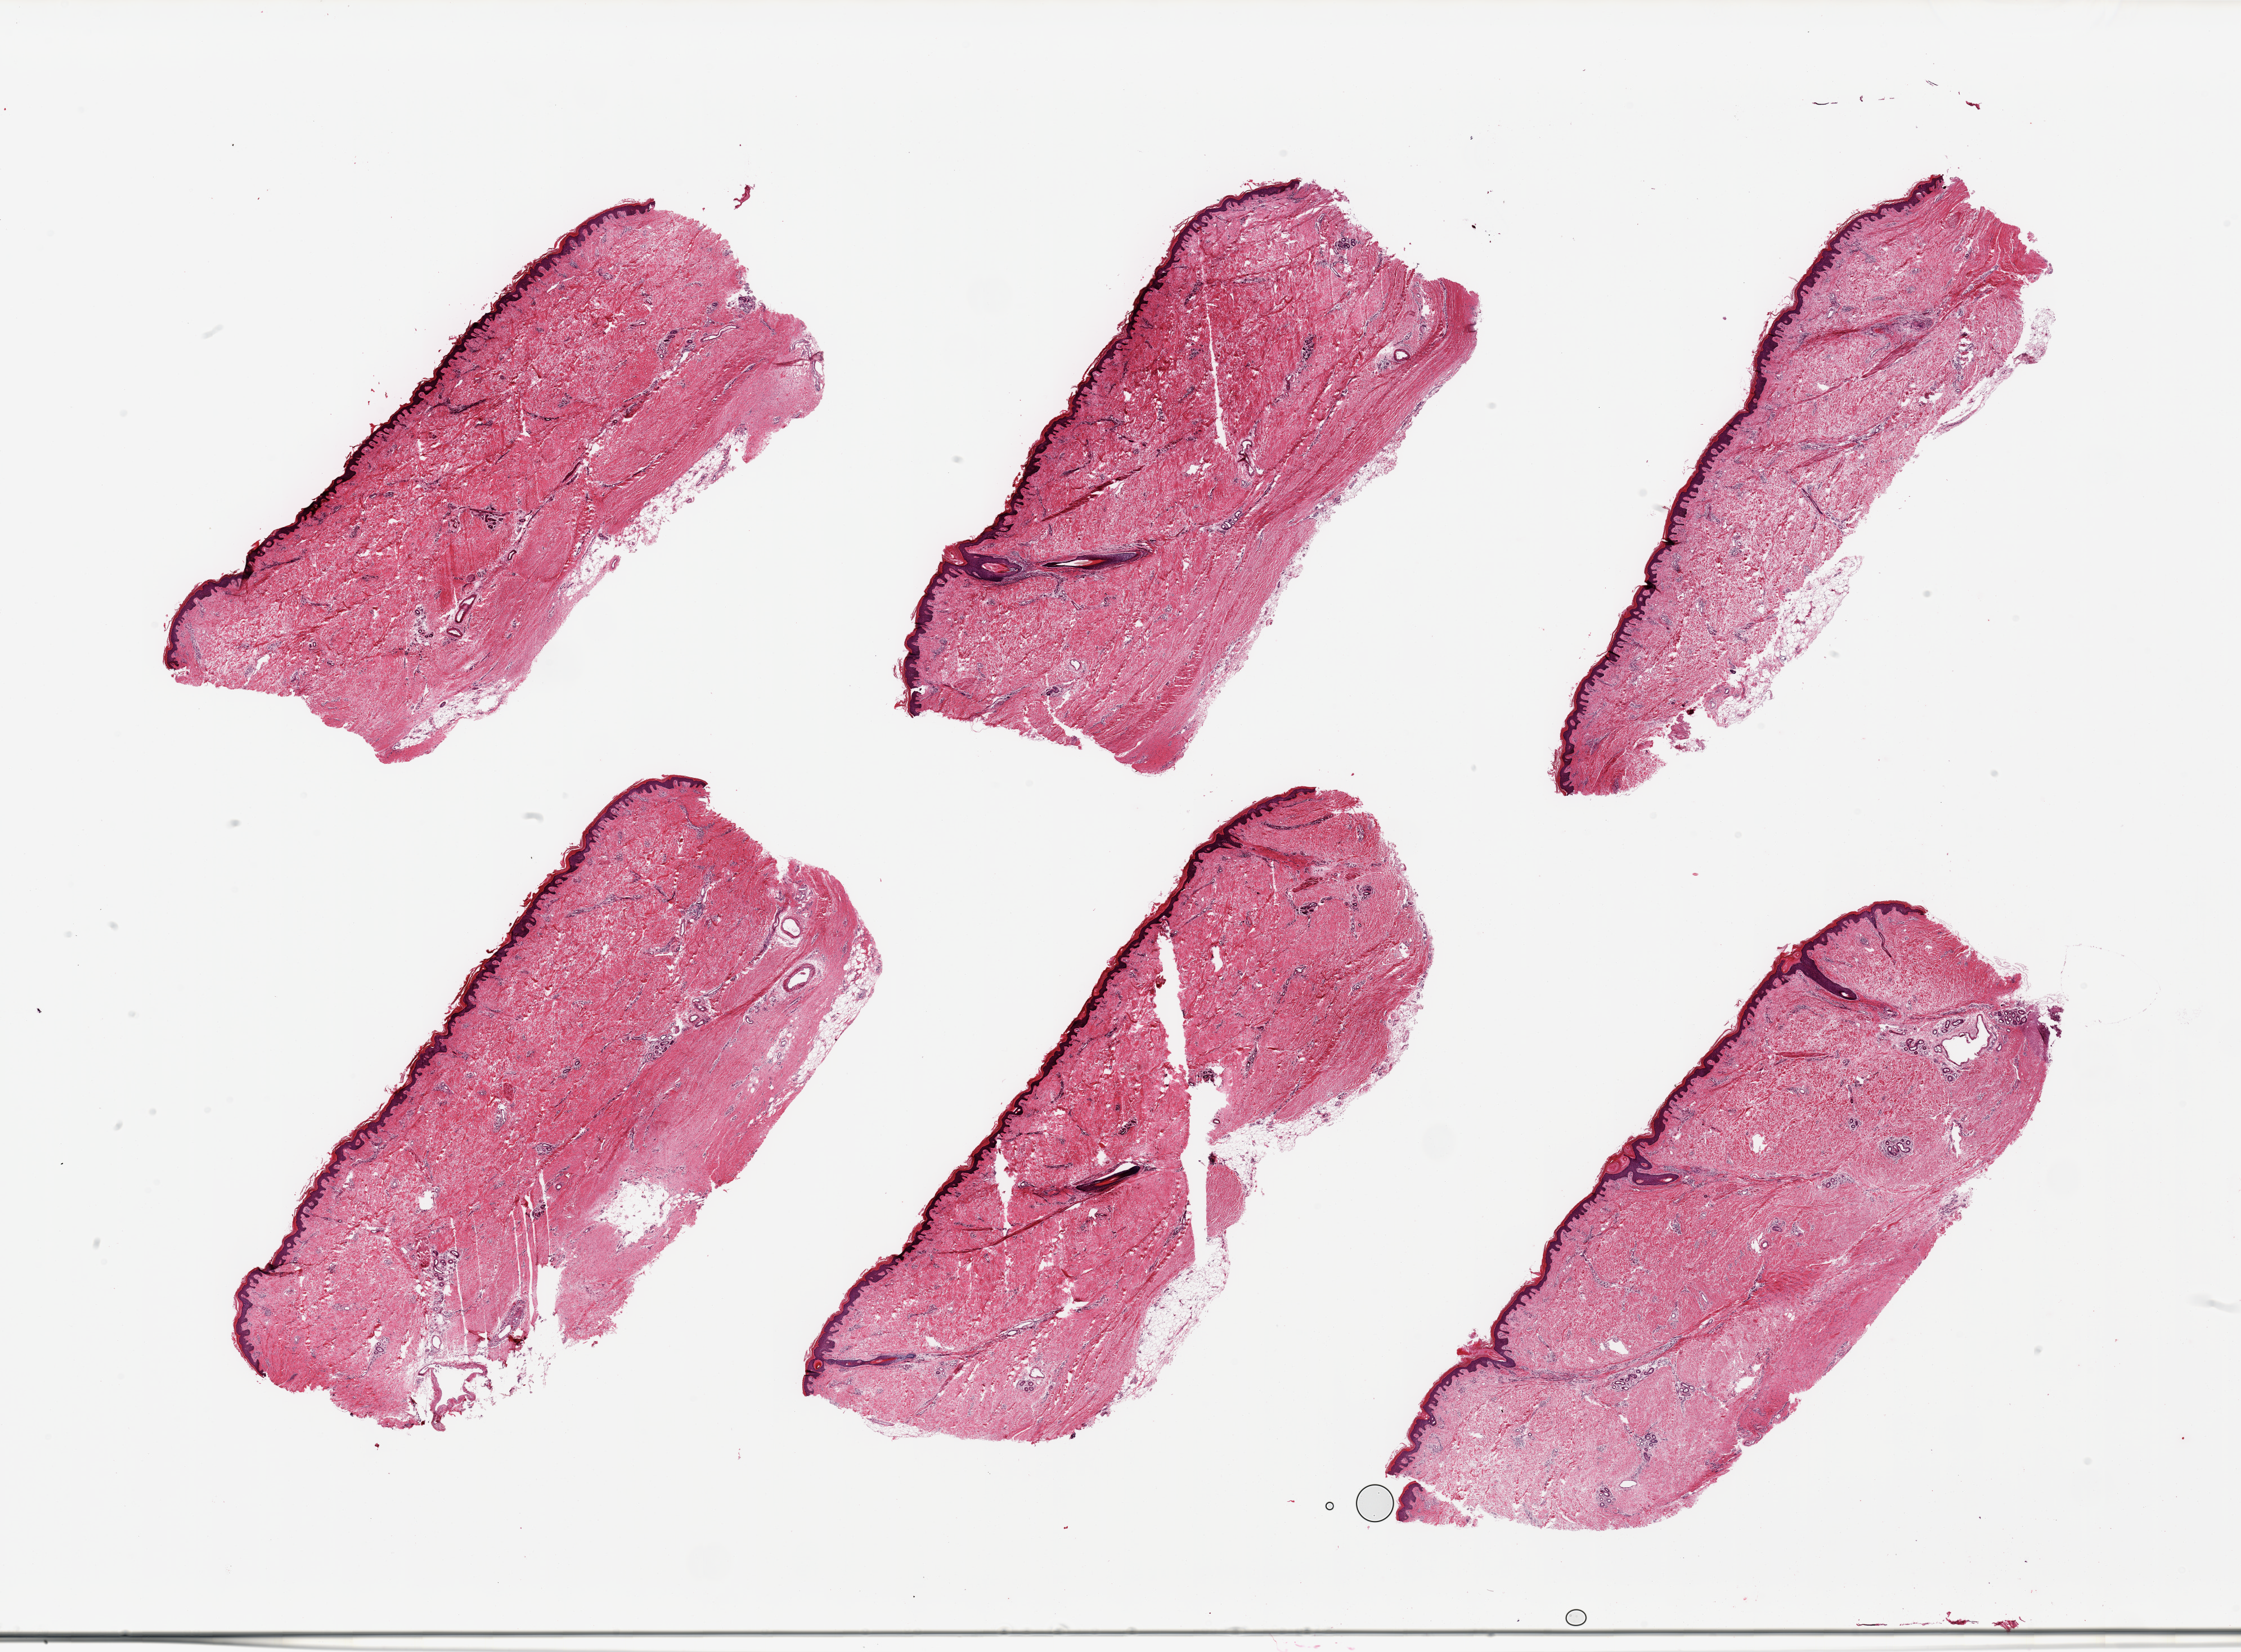
Whole-slide image, haematoxylin and eosin stain — whole scanned area (about 31.5 x 23.2 mm, acquisition: 20x scan) shown as a low-resolution overview. PAXgene-fixed paraffin-embedded (PFPE) section. Target tissue: skin of lower leg. Tissue donor sample.
Review note (as recorded): 6 pieces; thickened dermis with spindle cell proliferation c/w dialysis related nephrogenic fibrosing dermopathy; trace of adherent fat; ~46 microns epidermis.